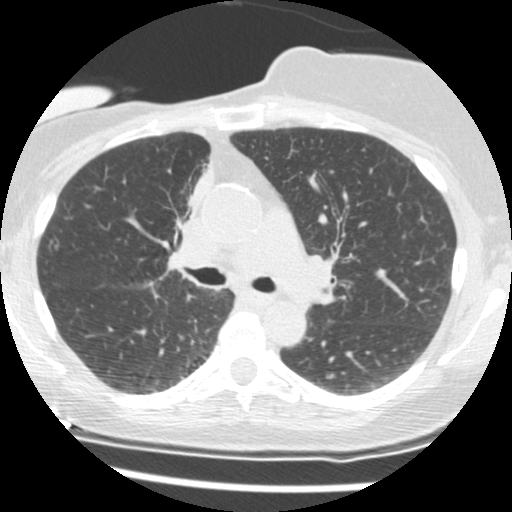
Low-dose screening chest CT, axial slice; second screening round (one year after baseline); lung window (W 1500 / L -600 HU); standard (soft-tissue) reconstruction kernel (STANDARD); slice 52 of 165 in the series; 512 × 512 image matrix. Female, age 56 years at enrolment.
Expert reader's lesion annotation, bounding box [x1, y1, x2, y2] px = [152, 167, 208, 259]. The screening reader recorded 2 non-calcified nodules or masses ≥4 mm on this exam (right middle lobe, right lower lobe); which of them this box marks is not recorded.